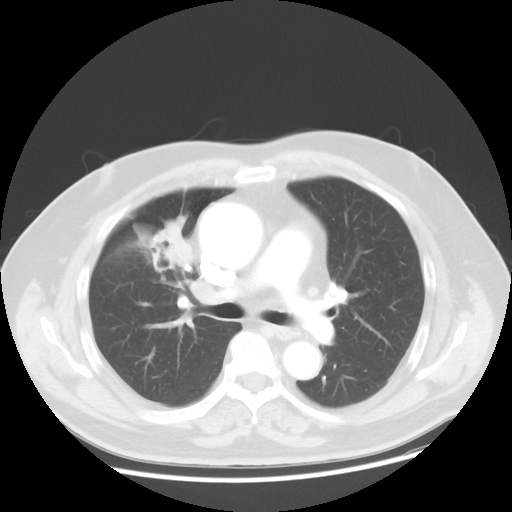
Chest CT, one axial slice. 120 kVp. Lung window (W 1500 / L -600 HU). 5 mm slice thickness. 512 × 512 image matrix, field of view 392 × 392 mm. Patient: male, 60 years. From the clinical record (not read from this slice): clinical TNM (as recorded): T2 N3 M0.
Annotated regions visible in this slice (rectangle marked by the reading radiologist):
- lung tumour (recorded histology: adenocarcinoma): bounding box (x1, y1, x2, y2) in pixels: (139, 205, 191, 286)